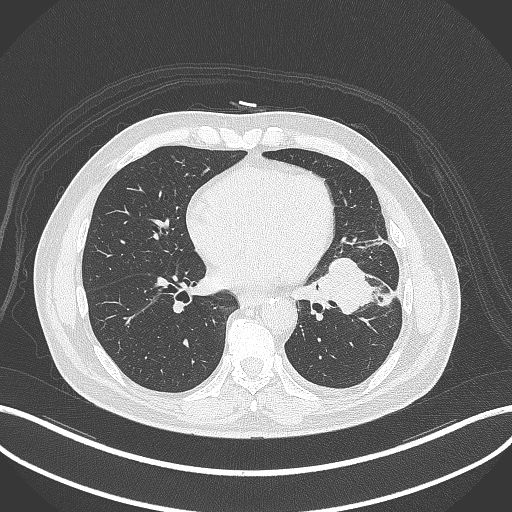
Chest CT, one axial slice. Position 149 of 230 along the scan axis. 120 kVp. Lung window (W 1500 / L -600 HU). 512 × 512 image matrix. Male patient, age 68 years. From the clinical record (not read from this slice): clinical TNM (as recorded): T2b N0 M0.
Outlined on this slice (bounding box drawn by a radiologist):
- lung tumour (recorded histology: squamous cell carcinoma): box from (x=311, y=255) to (x=375, y=319) px